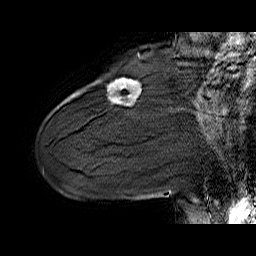
Breast MRI (dynamic contrast-enhanced), one sagittal slice. Slice 16 of 60 in the series (ordered by position). Dynamic contrast-enhanced series, time point 2 of 6 at this slice position (early post-contrast). 1.5 T. TE 6.4 ms, TR 32.9 ms. 4 mm slice thickness. 256 × 256 image matrix, field of view 200 × 200 mm. Female patient. From the clinical record (not read from this slice): setting: breast cancer imaged before/during neoadjuvant chemotherapy; receptor status: HER2-positive.
Outlined on this slice (semi-automatic segmentation, software-assisted and operator-edited):
- analysis volume of interest (the breast-tissue region the enhancement analysis was run in; not a lesion): bounding box (x1, y1, x2, y2) in pixels: (108, 79, 141, 106)
- tumour enhancement mask (voxels above the 100 % enhancement threshold inside the analysis volume of interest): (117, 79, 134, 83)